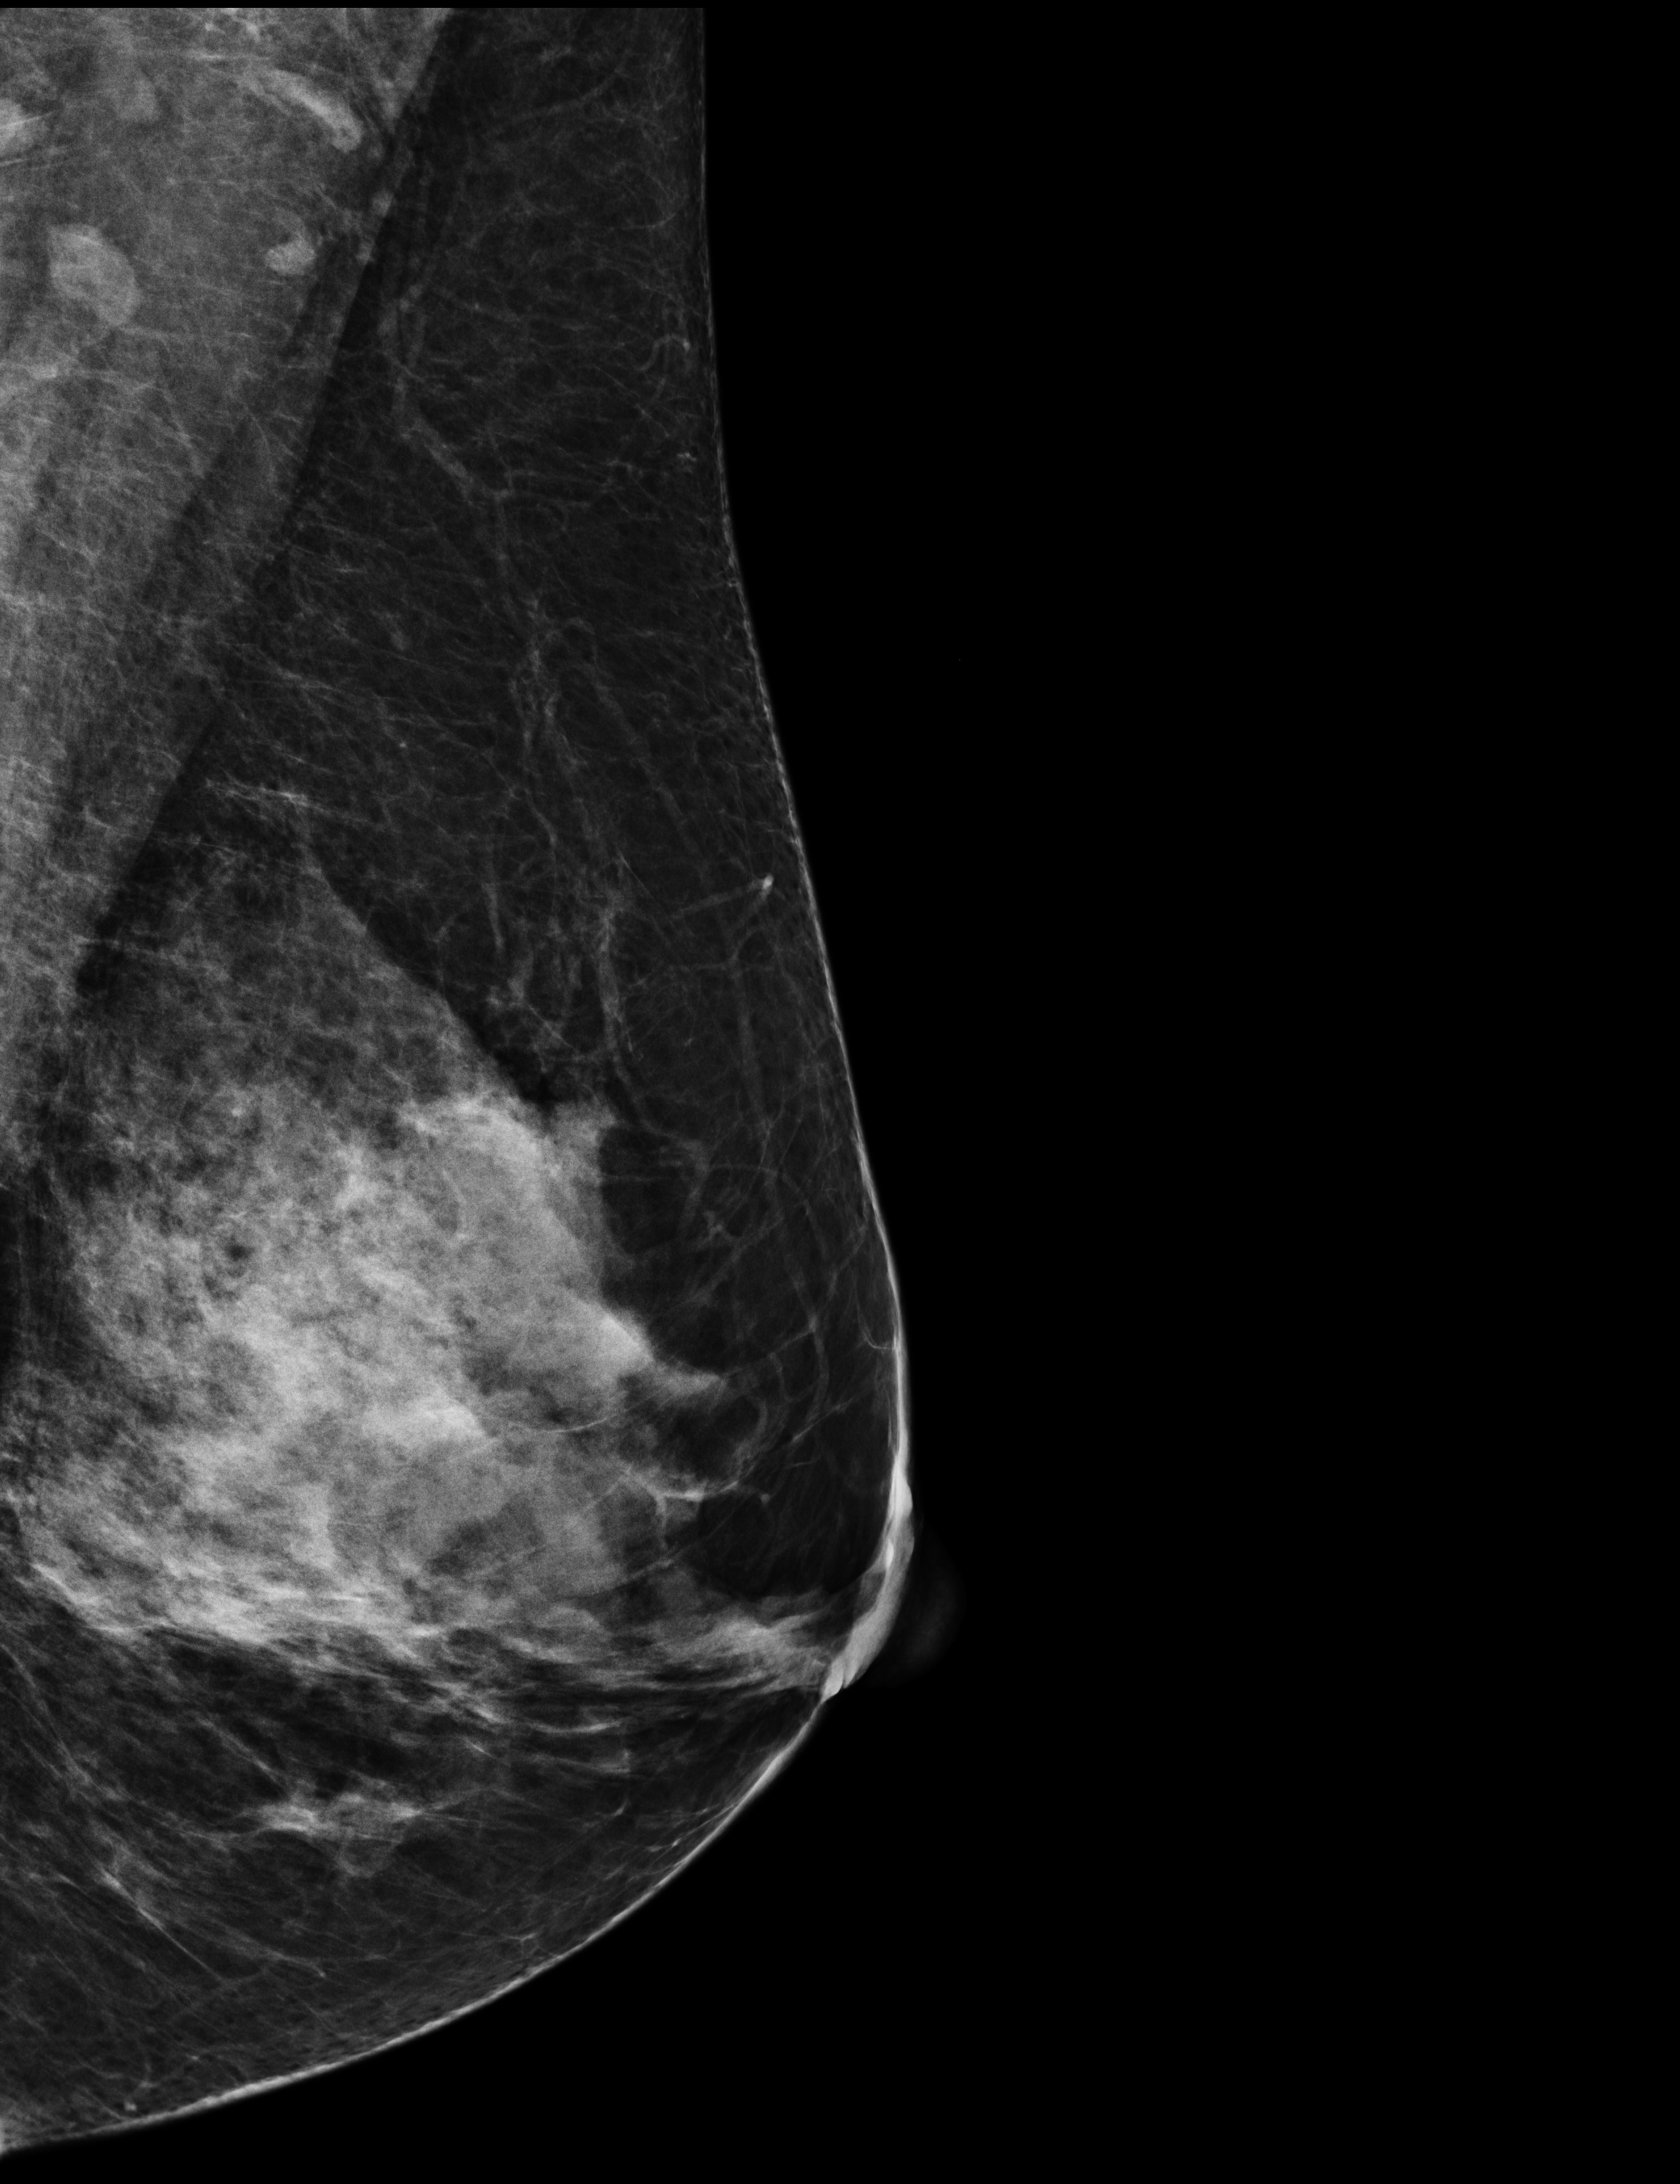
Annual screening mammography examination, compressed breast thickness 68 mm, system: Selenia Dimensions. Patient aged 51 years (female).
Image type: full-field digital mammogram. Breast: left. Projection: MLO view.